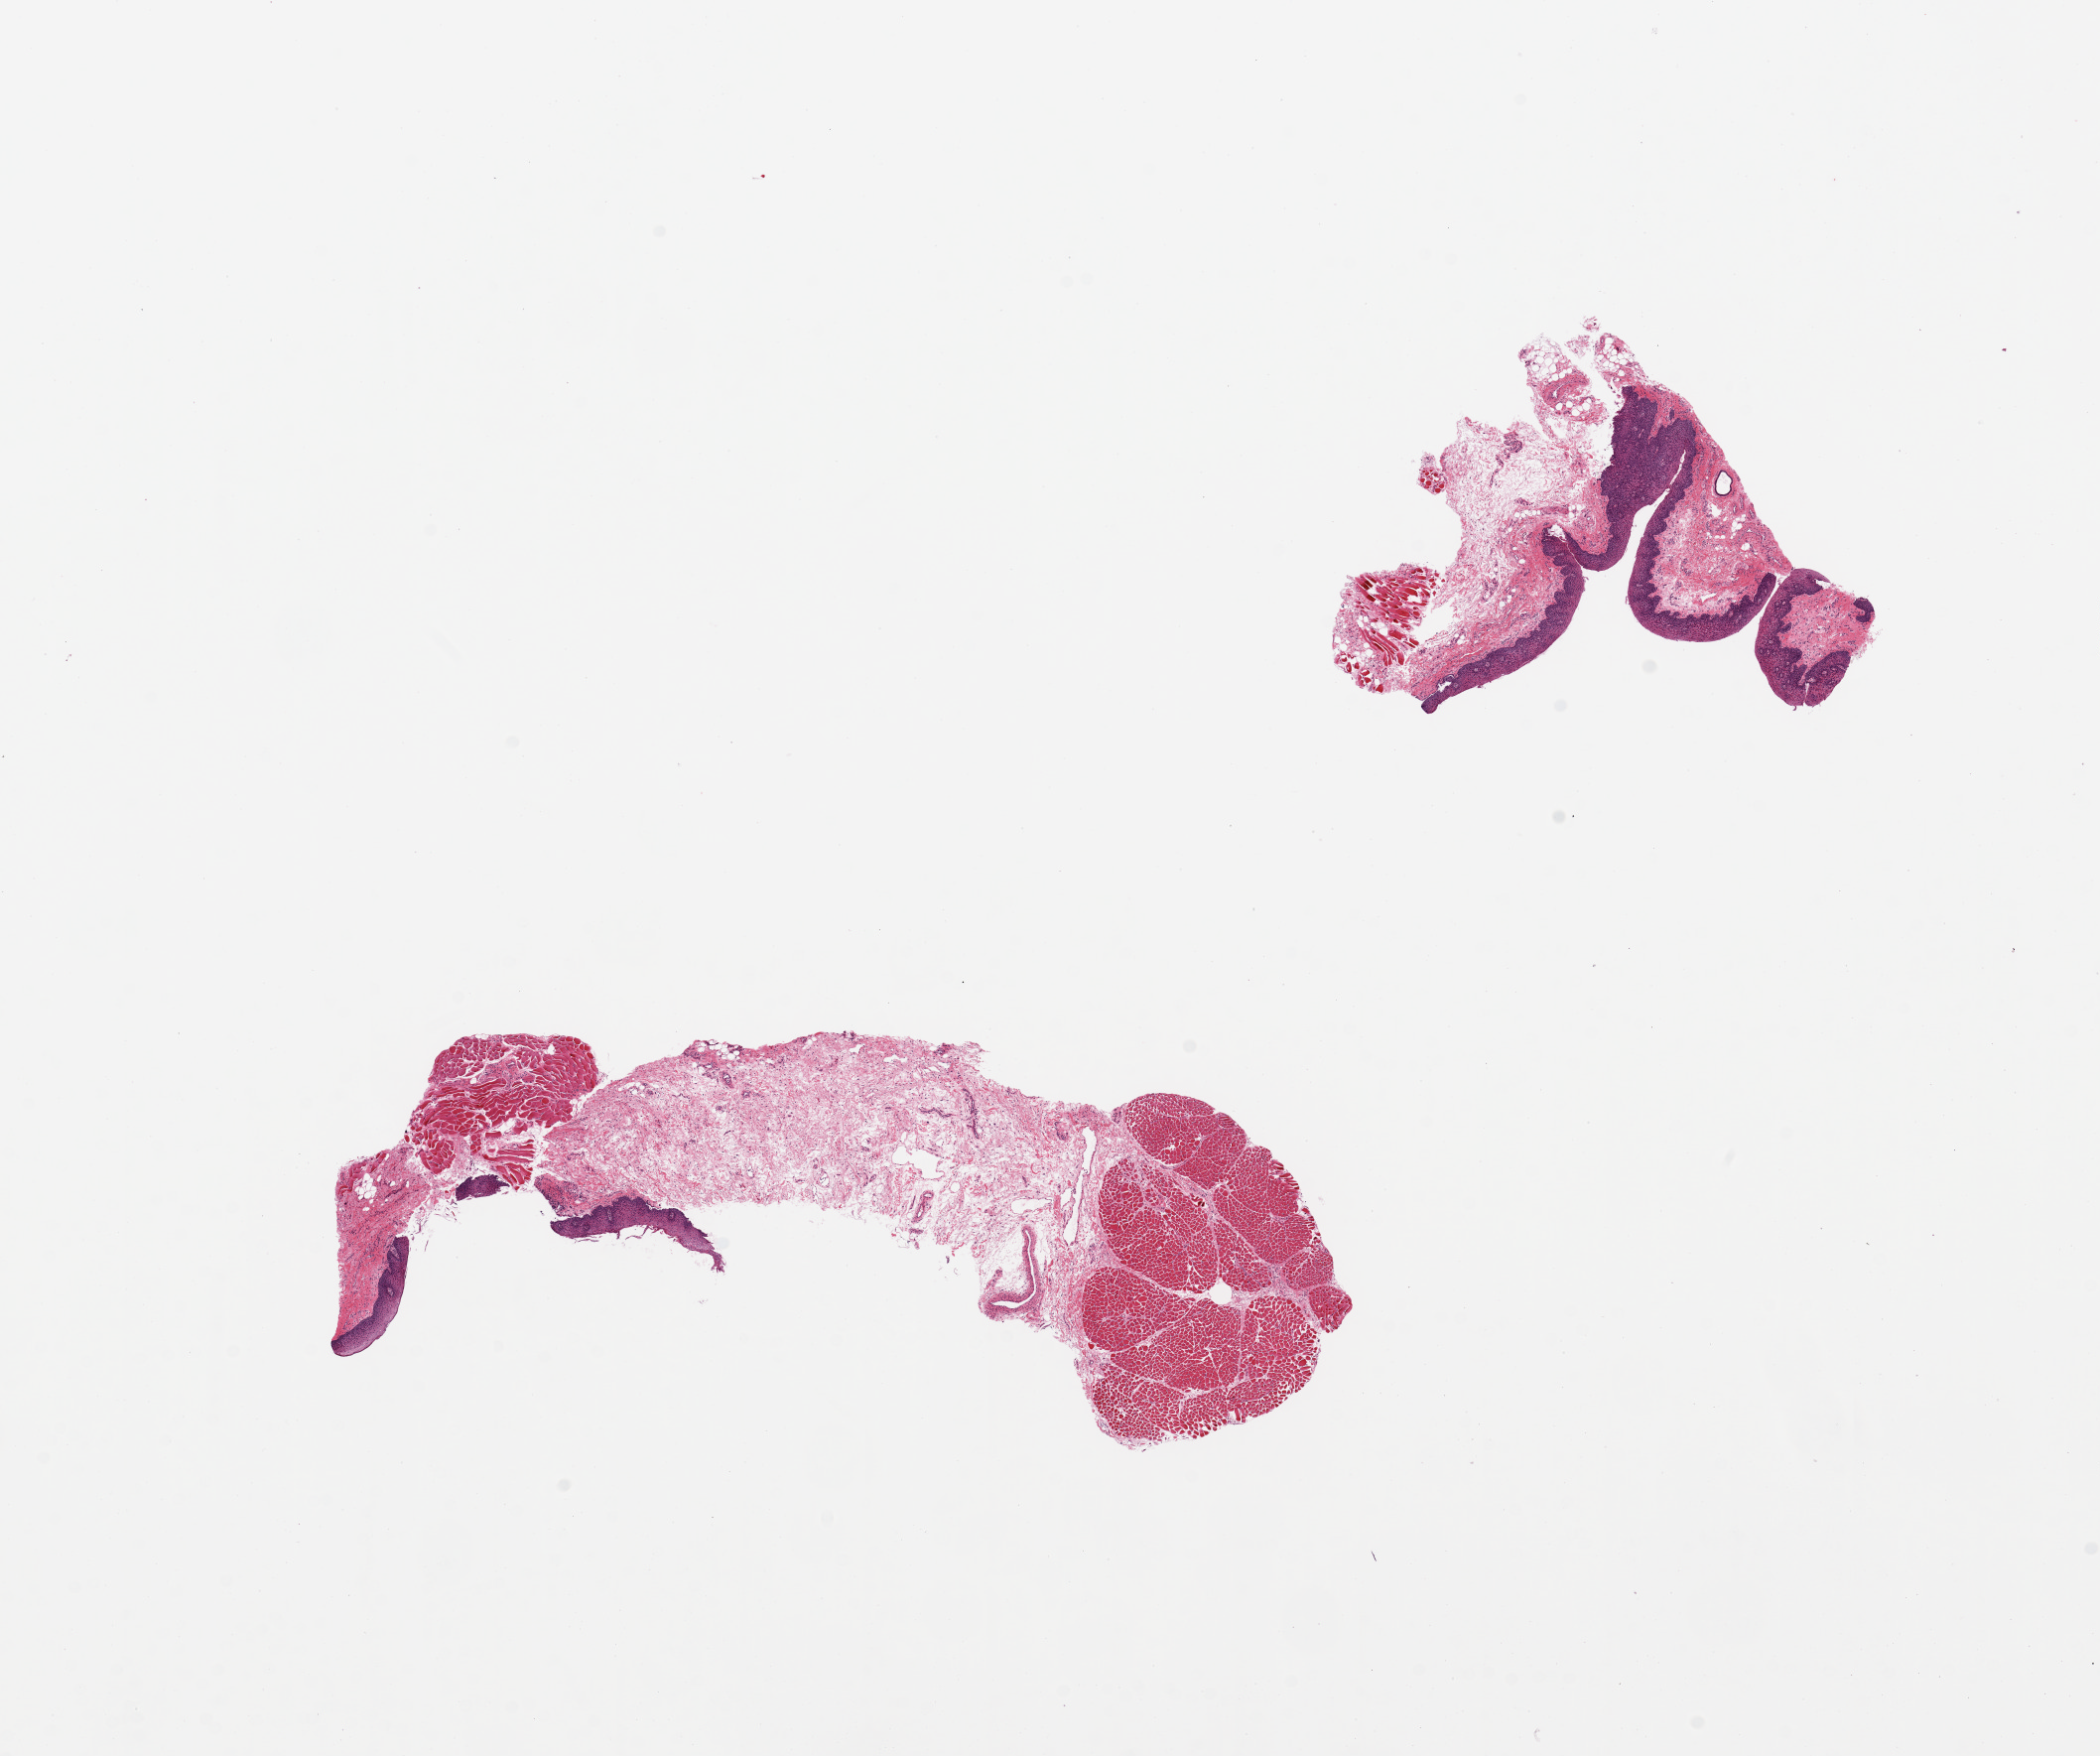
Whole-slide image, haematoxylin and eosin stain — low-resolution overview of the scanned area, about 16.7 x 14.0 mm. PAXgene-fixed, paraffin-embedded tissue. Target tissue: minor salivary gland. Tissue donor sample. Donor: female.
Review note (as recorded): 2 pieces, no salivary gland tissue present, specimen consists of squamous mucosa, stroma and skeletal muscle.